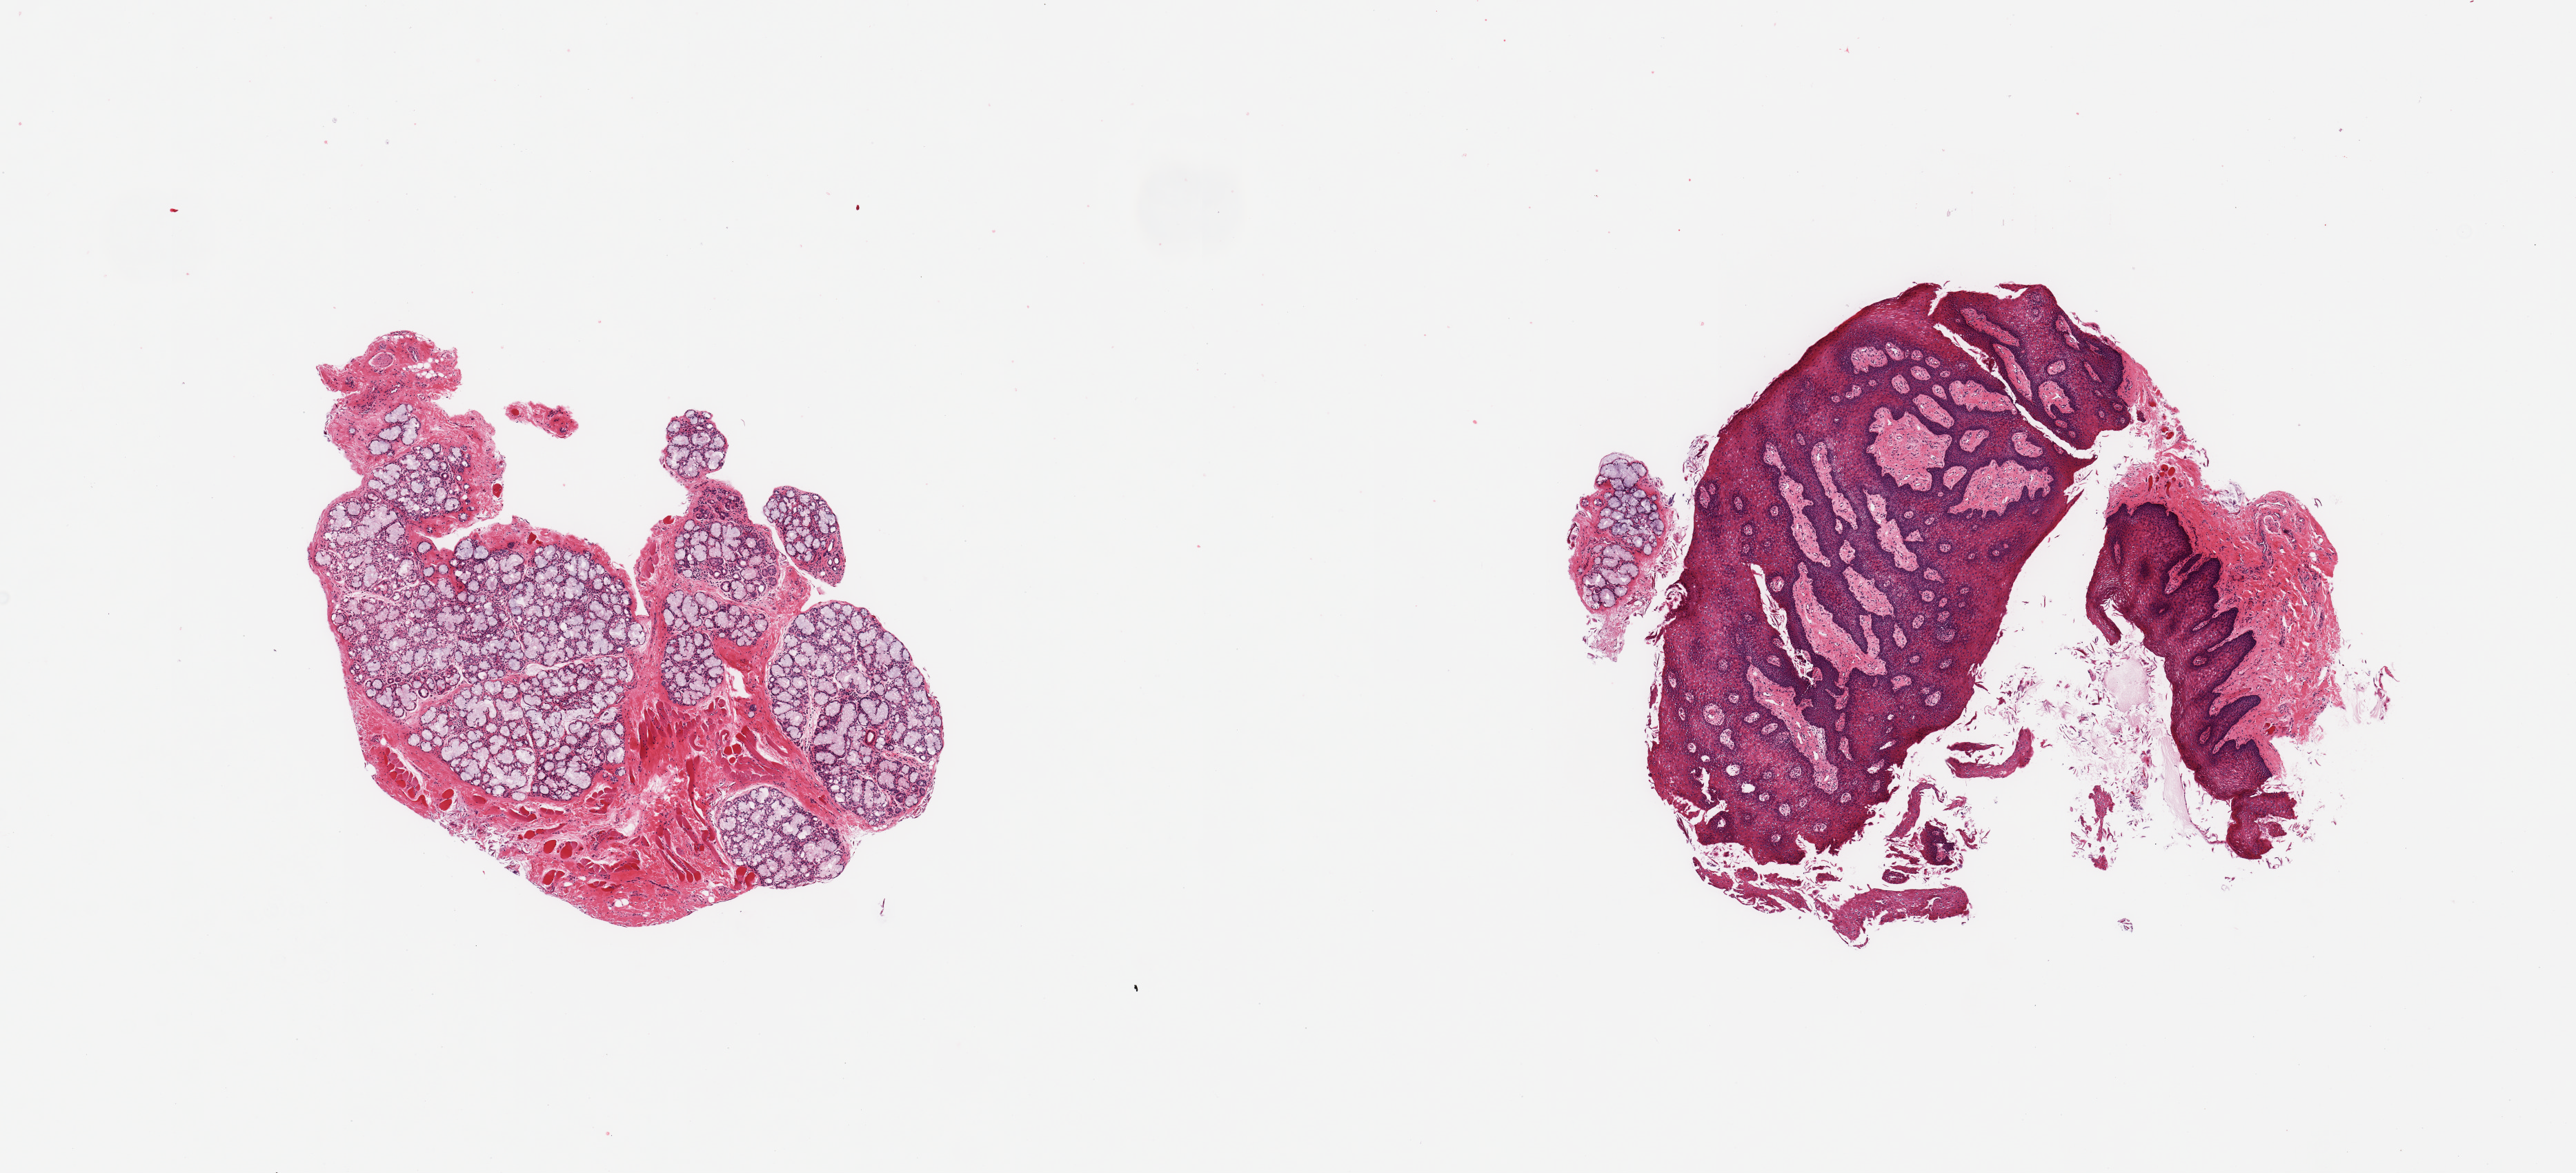
Digitized H&E-stained section, shown as a low-resolution overview of the whole scanned area (about 14.8 x 6.7 mm). Donor sex: male.
Specimen: PAXgene-fixed paraffin-embedded (PFPE) section; section of minor salivary gland (target tissue); donor tissue sample.